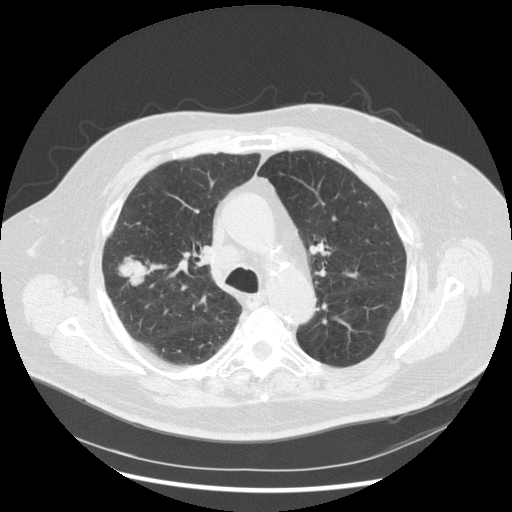
Low-dose screening chest CT, axial slice; third annual screen; lung window (W 1500 / L -600 HU); 2.5 mm slice thickness; slice 190 of 263 in the series. Male participant, aged 72 years at enrolment. Former smoker at enrolment.
Expert-annotated lung lesion, bounding box <101,250,157,298> (left, top, right, bottom; pixels). The exam's reader record, not a measurement of the box and not confirmed to be the same lesion: non-calcified nodule or mass ≥4 mm, right upper lobe, 31 × 31 mm, poorly defined margins, soft tissue attenuation, pre-existing on the prior screen: no.